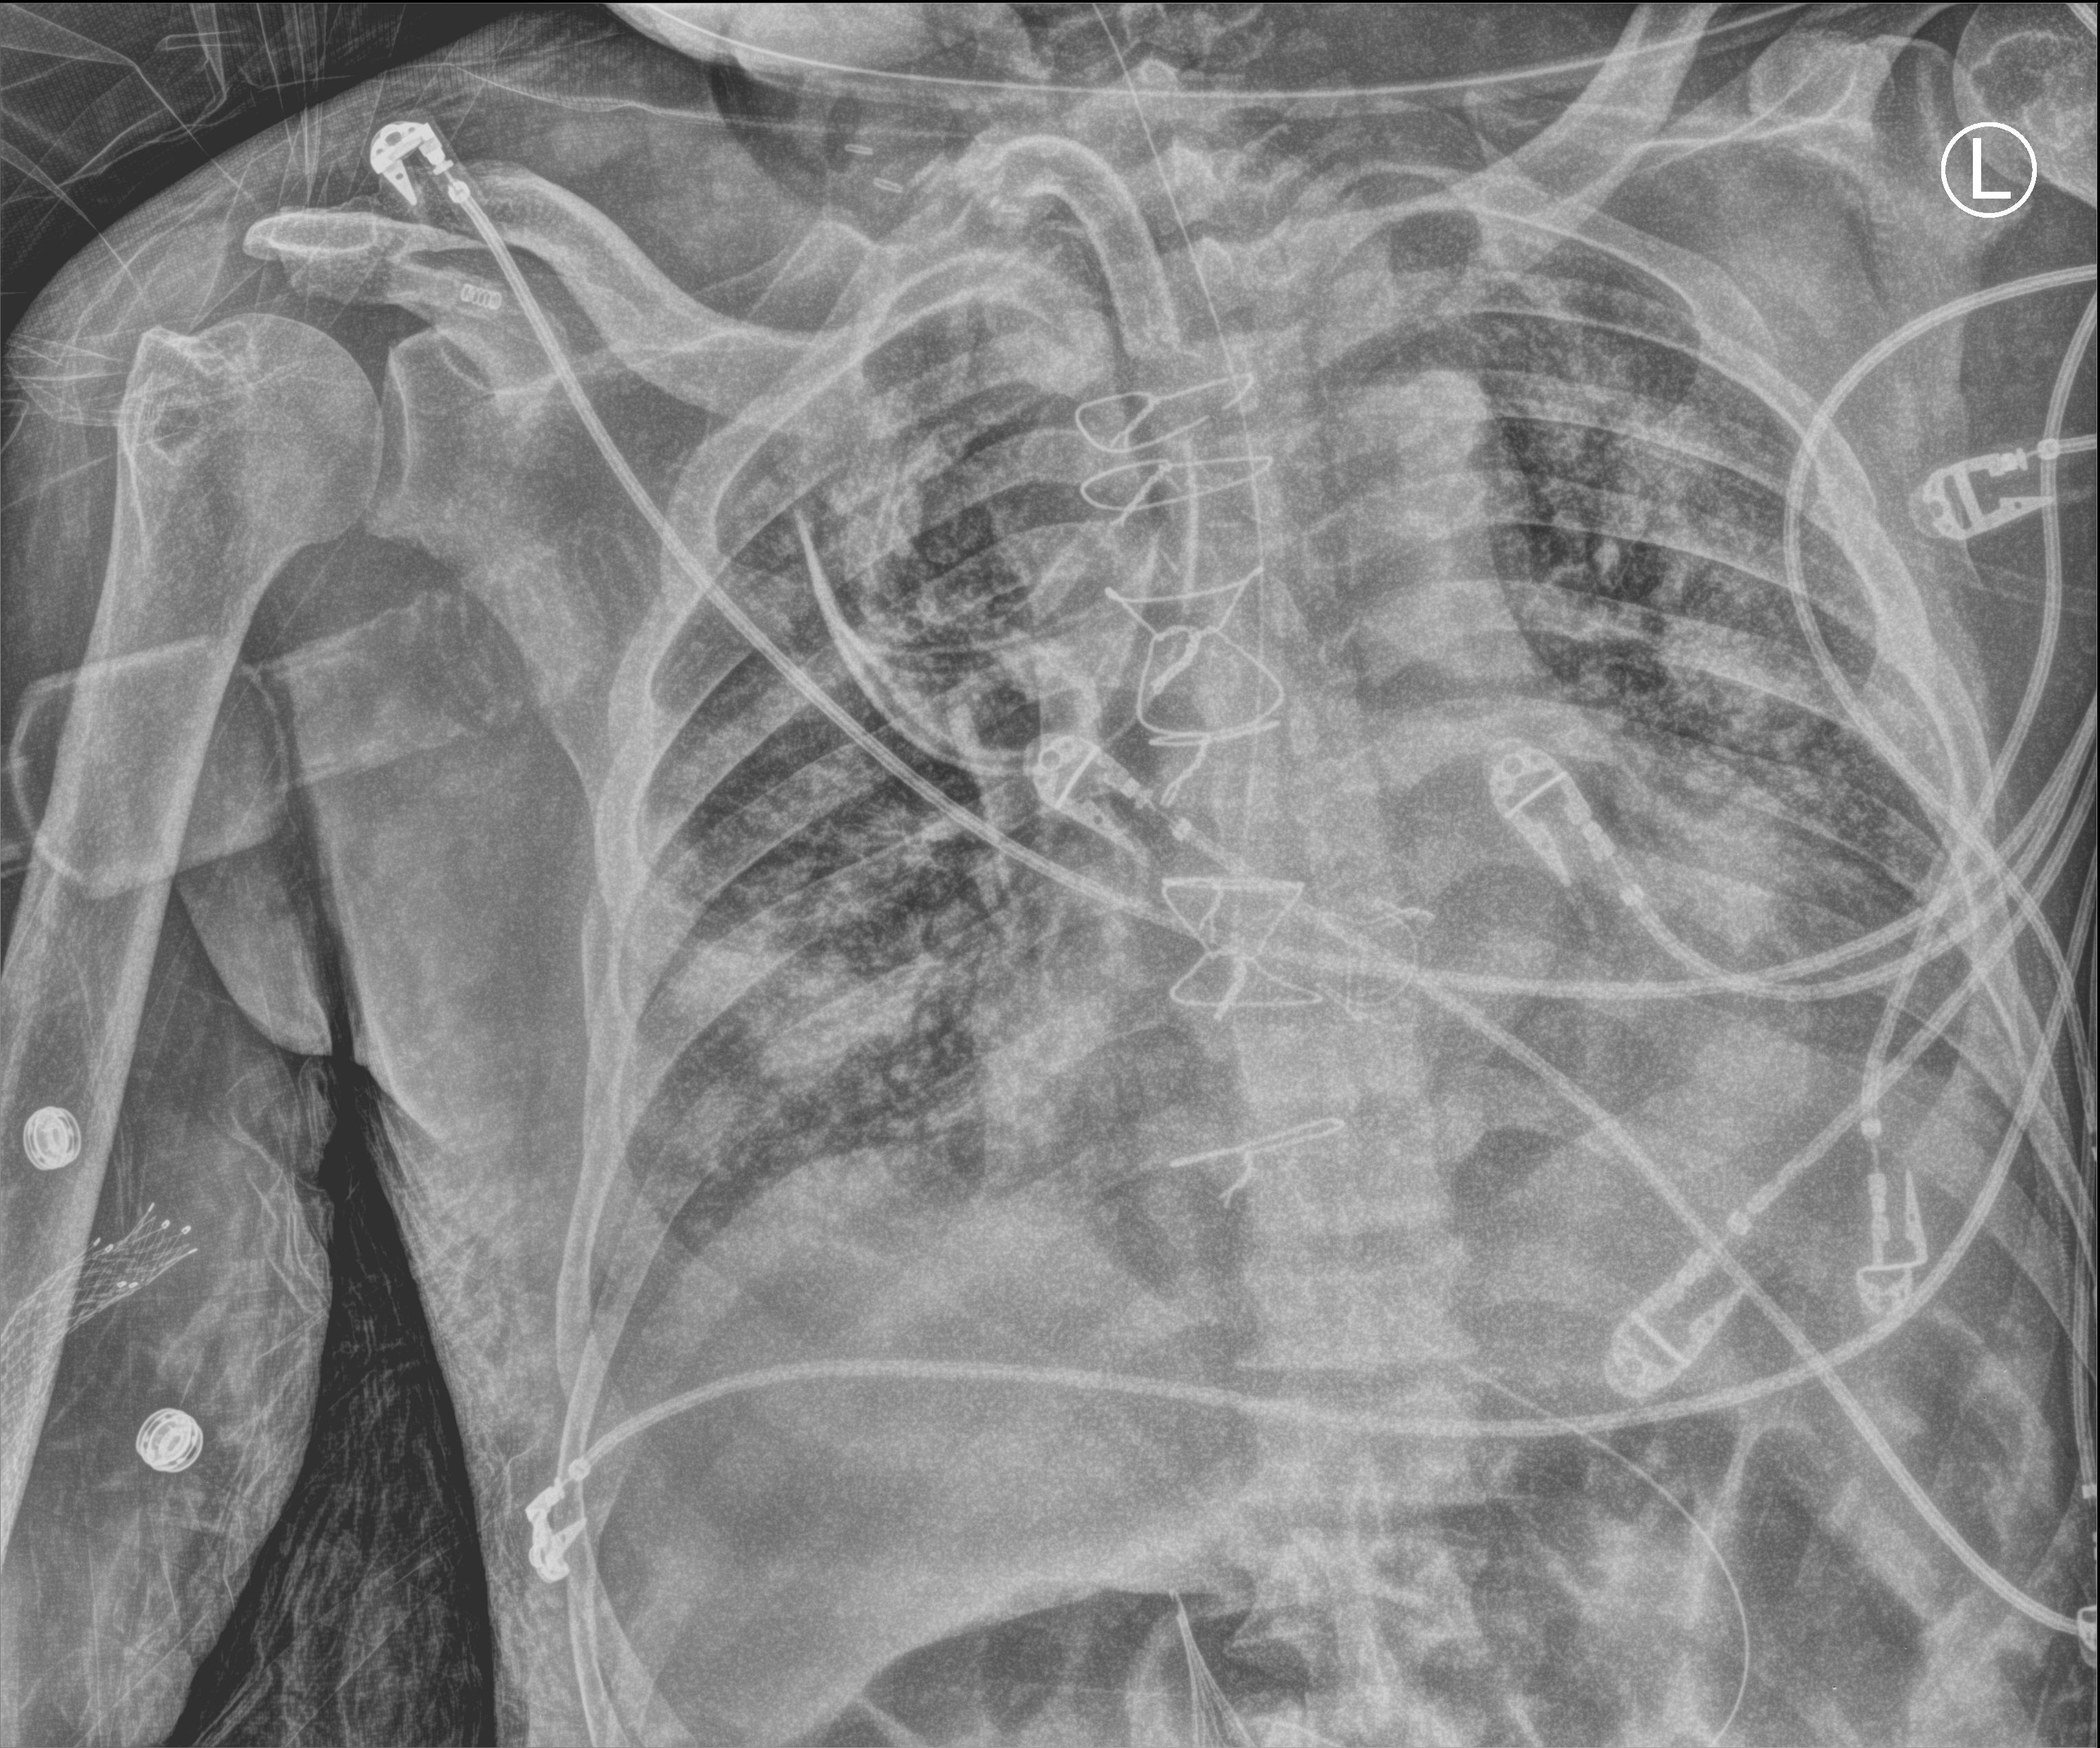
Chest X-ray (portable), anteroposterior (AP) projection. Male patient hospitalised with COVID-19, age 60–74 years.
From the hospital-stay record, not from the radiograph (when in the stay this image was taken is not recorded):
- admitted to intensive care during this hospital stay: yes
- mechanically ventilated during this hospital stay: yes
- length of hospital stay: 50 days